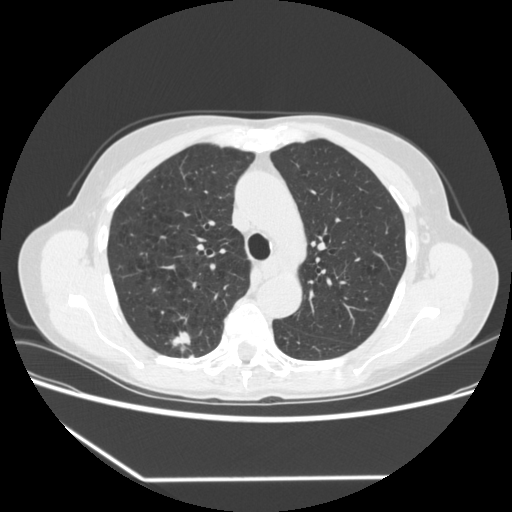
Low-dose screening chest CT, one axial slice. Slice 237 of 323 in the series (ordered by position). Reconstruction kernel STANDARD. Lung window (W 1500 / L -600 HU). 512 × 512 image matrix, field of view 360 × 360 mm.
Outlined on this slice (expert manual segmentation):
- lesion 1 (tumor, upper lobe of right lung): bounding box <172,331,191,352> (left, top, right, bottom; pixels)